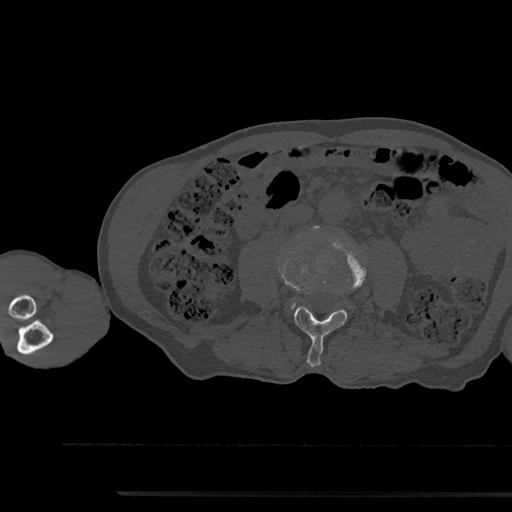
CT including the spine, one axial slice. Position 461 of 797 along the scan axis. 120 kVp. Bone window (W 1800 / L 400 HU). 0.5 mm slice thickness. 512 × 512 image matrix, field of view 367 × 367 mm. Male patient, age 79 years. Case-level facts recorded for this patient, not image findings: primary cancer: prostate.
Outlined on this slice (semi-automatically segmented with operator editing):
- L3 vertebra: bounding box <294,238,366,367> (left, top, right, bottom; pixels)
- L4 vertebra: <292,303,295,307>